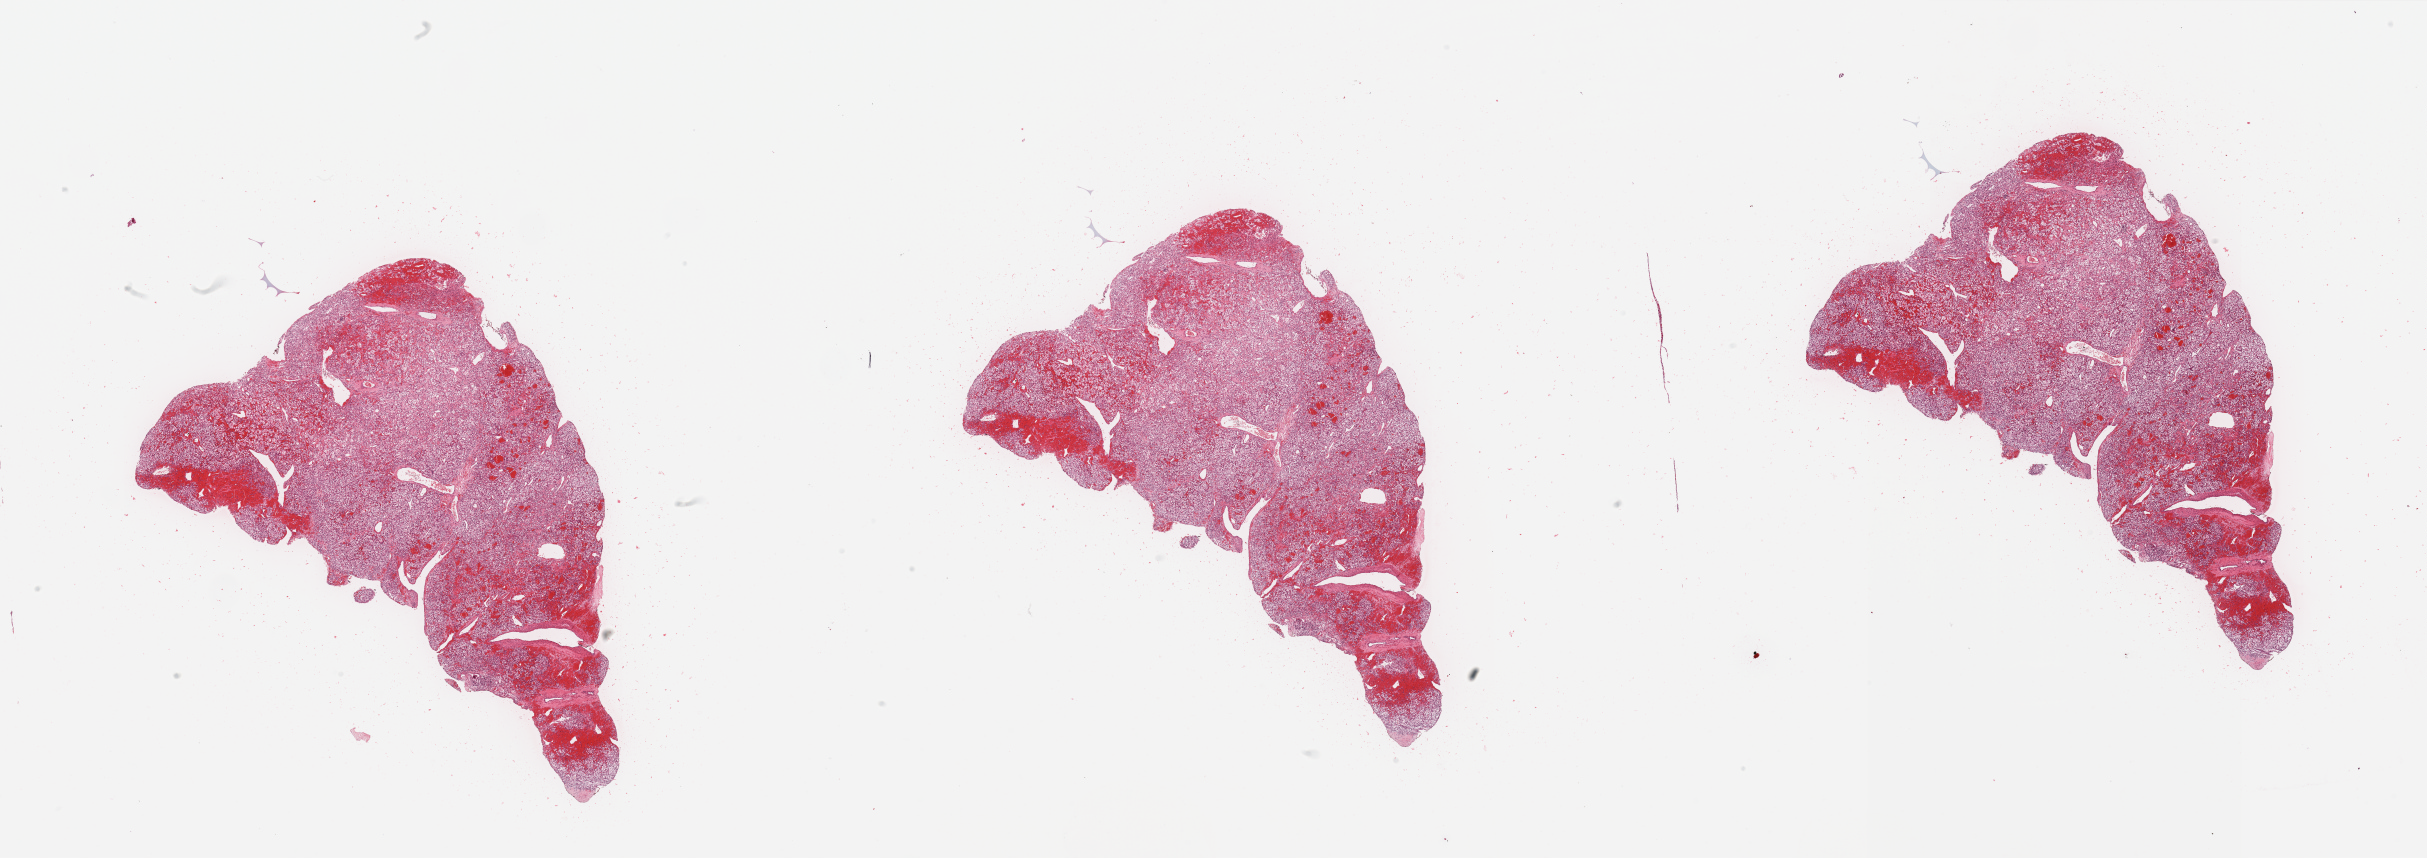
Whole-slide histology image, H&E-stained — shown as a low-resolution overview of the whole scanned area (about 38.4 x 13.6 mm, acquisition: 20x scan); tumour tissue sample, sampled site: kidney. 62-year-old male patient. Histologic grade: G3 (poorly differentiated). Pathologist review of this section (percent, as recorded): tumour nuclei 90%, necrosis 1%.
* primary tumour site (as recorded): lower pole
* diagnosis: Renal cell carcinoma, NOS